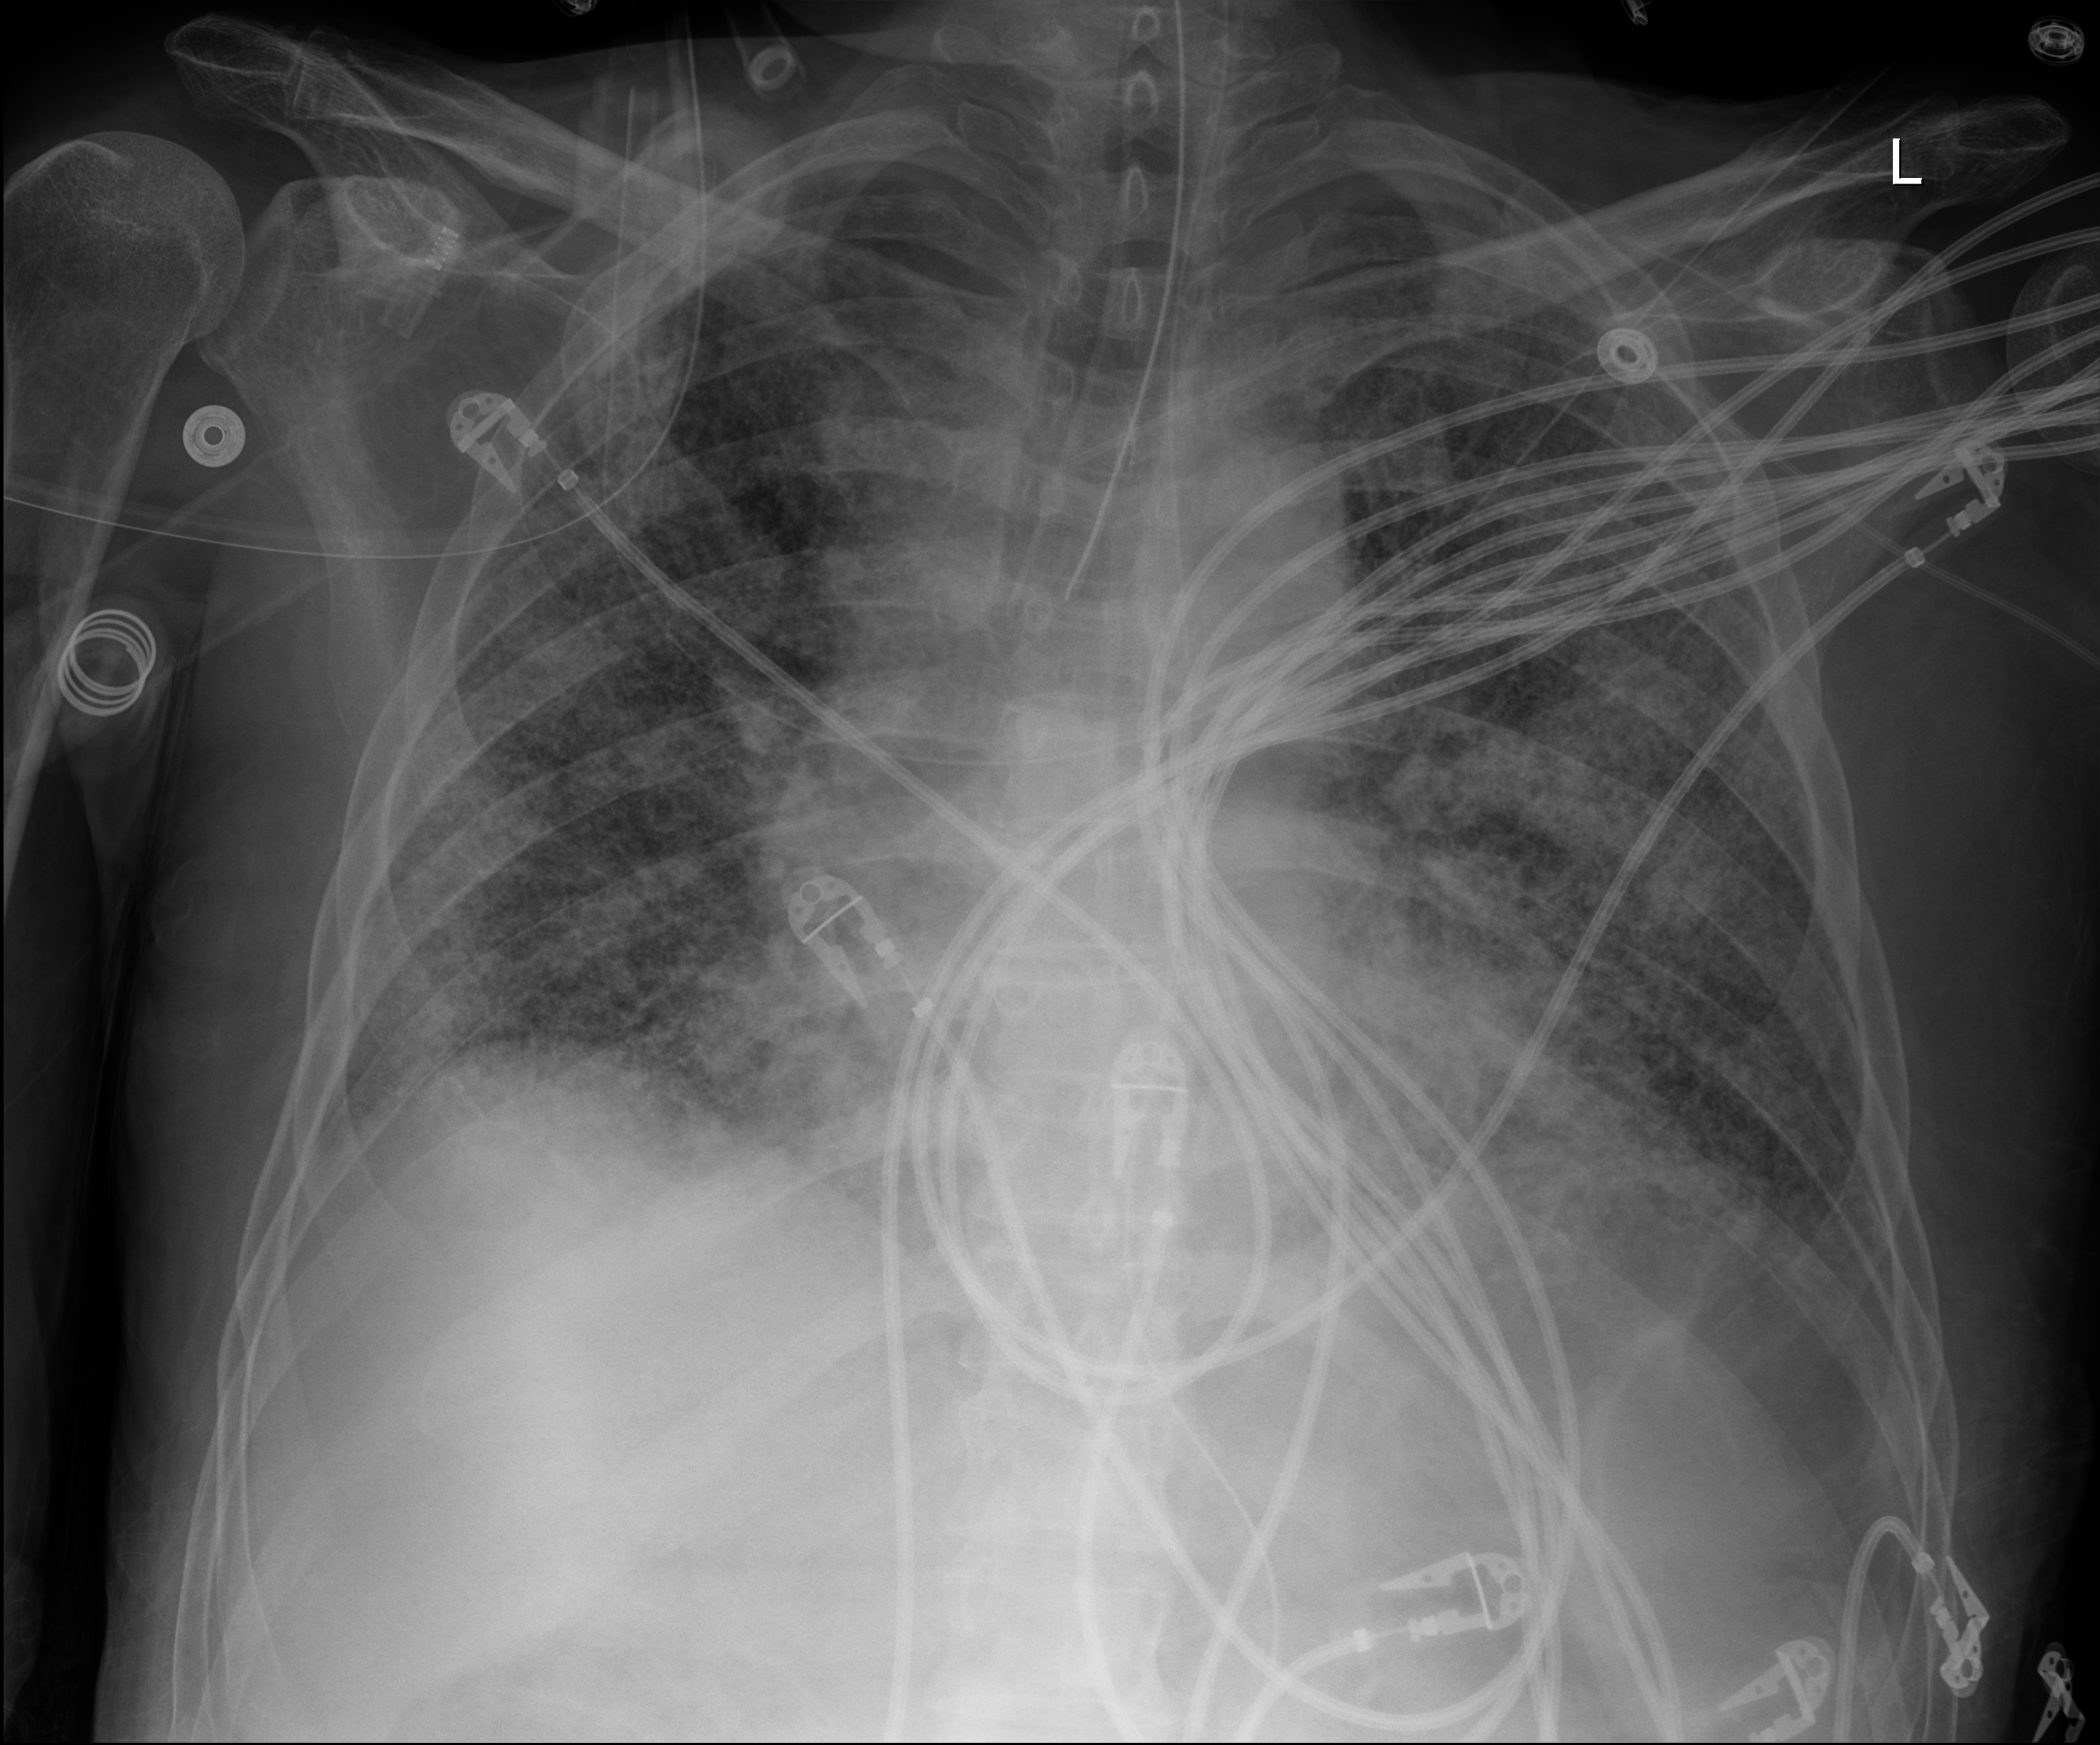
Bedside chest radiograph (digital radiography); anteroposterior (AP) projection. Patient hospitalised with COVID-19; male, aged 60–74 years.
Hospital-stay facts (about this admission, not read from this image; timing relative to this image not recorded):
- admitted to intensive care during this hospital stay: yes